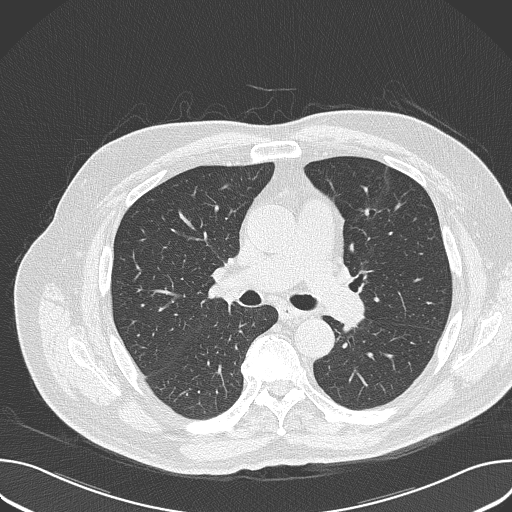
Low-dose screening chest CT, axial slice, baseline screening round, lung window (W 1500 / L -600 HU), 2 mm slice thickness, lung (sharp) reconstruction kernel (B50f), 120 kVp. Male participant, aged 74 years at enrolment. Former smoker at enrolment.
Lesion marked by an expert reader, bounding box (x1, y1, x2, y2) in pixels: (344, 194, 385, 238). The screening reader recorded 2 non-calcified nodules or masses ≥4 mm on this exam; which of them this box marks is not recorded. Official screen result: positive, change unspecified: nodule(s) >= 4 mm or enlarging nodule(s), mass(es), or other non-specific abnormalities suspicious for lung cancer. Later outcome: lung cancer diagnosed 1049 days after this screen (after the third annual screen) — adenocarcinoma, NOS, left upper lobe, poorly differentiated (G3), stage IIIA (AJCC 6th edition), 27 mm at pathology.